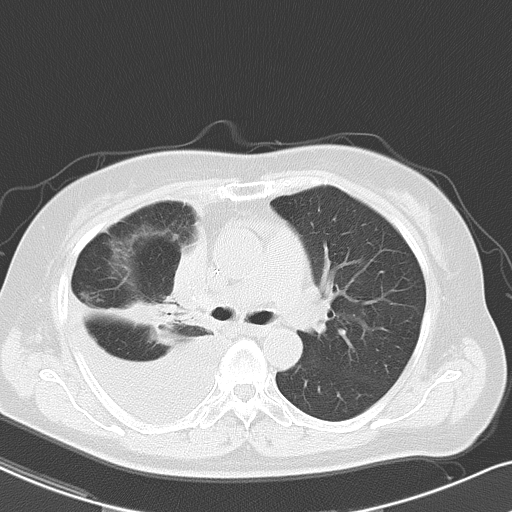
Chest CT, one axial slice. Position 32 of 48 along the scan axis. Reconstruction kernel B70f. Lung window (W 1500 / L -600 HU). 5 mm slice thickness. 512 × 512 image matrix, field of view 328 × 328 mm. Patient: female, 69 years. Case-level facts recorded for this patient, not image findings: clinical TNM (as recorded): T2a N0 M1c.
Annotated regions visible in this slice (bounding box drawn by a radiologist):
- lung tumour (recorded histology: adenocarcinoma): bounding box [x1, y1, x2, y2] px = [164, 219, 212, 318]